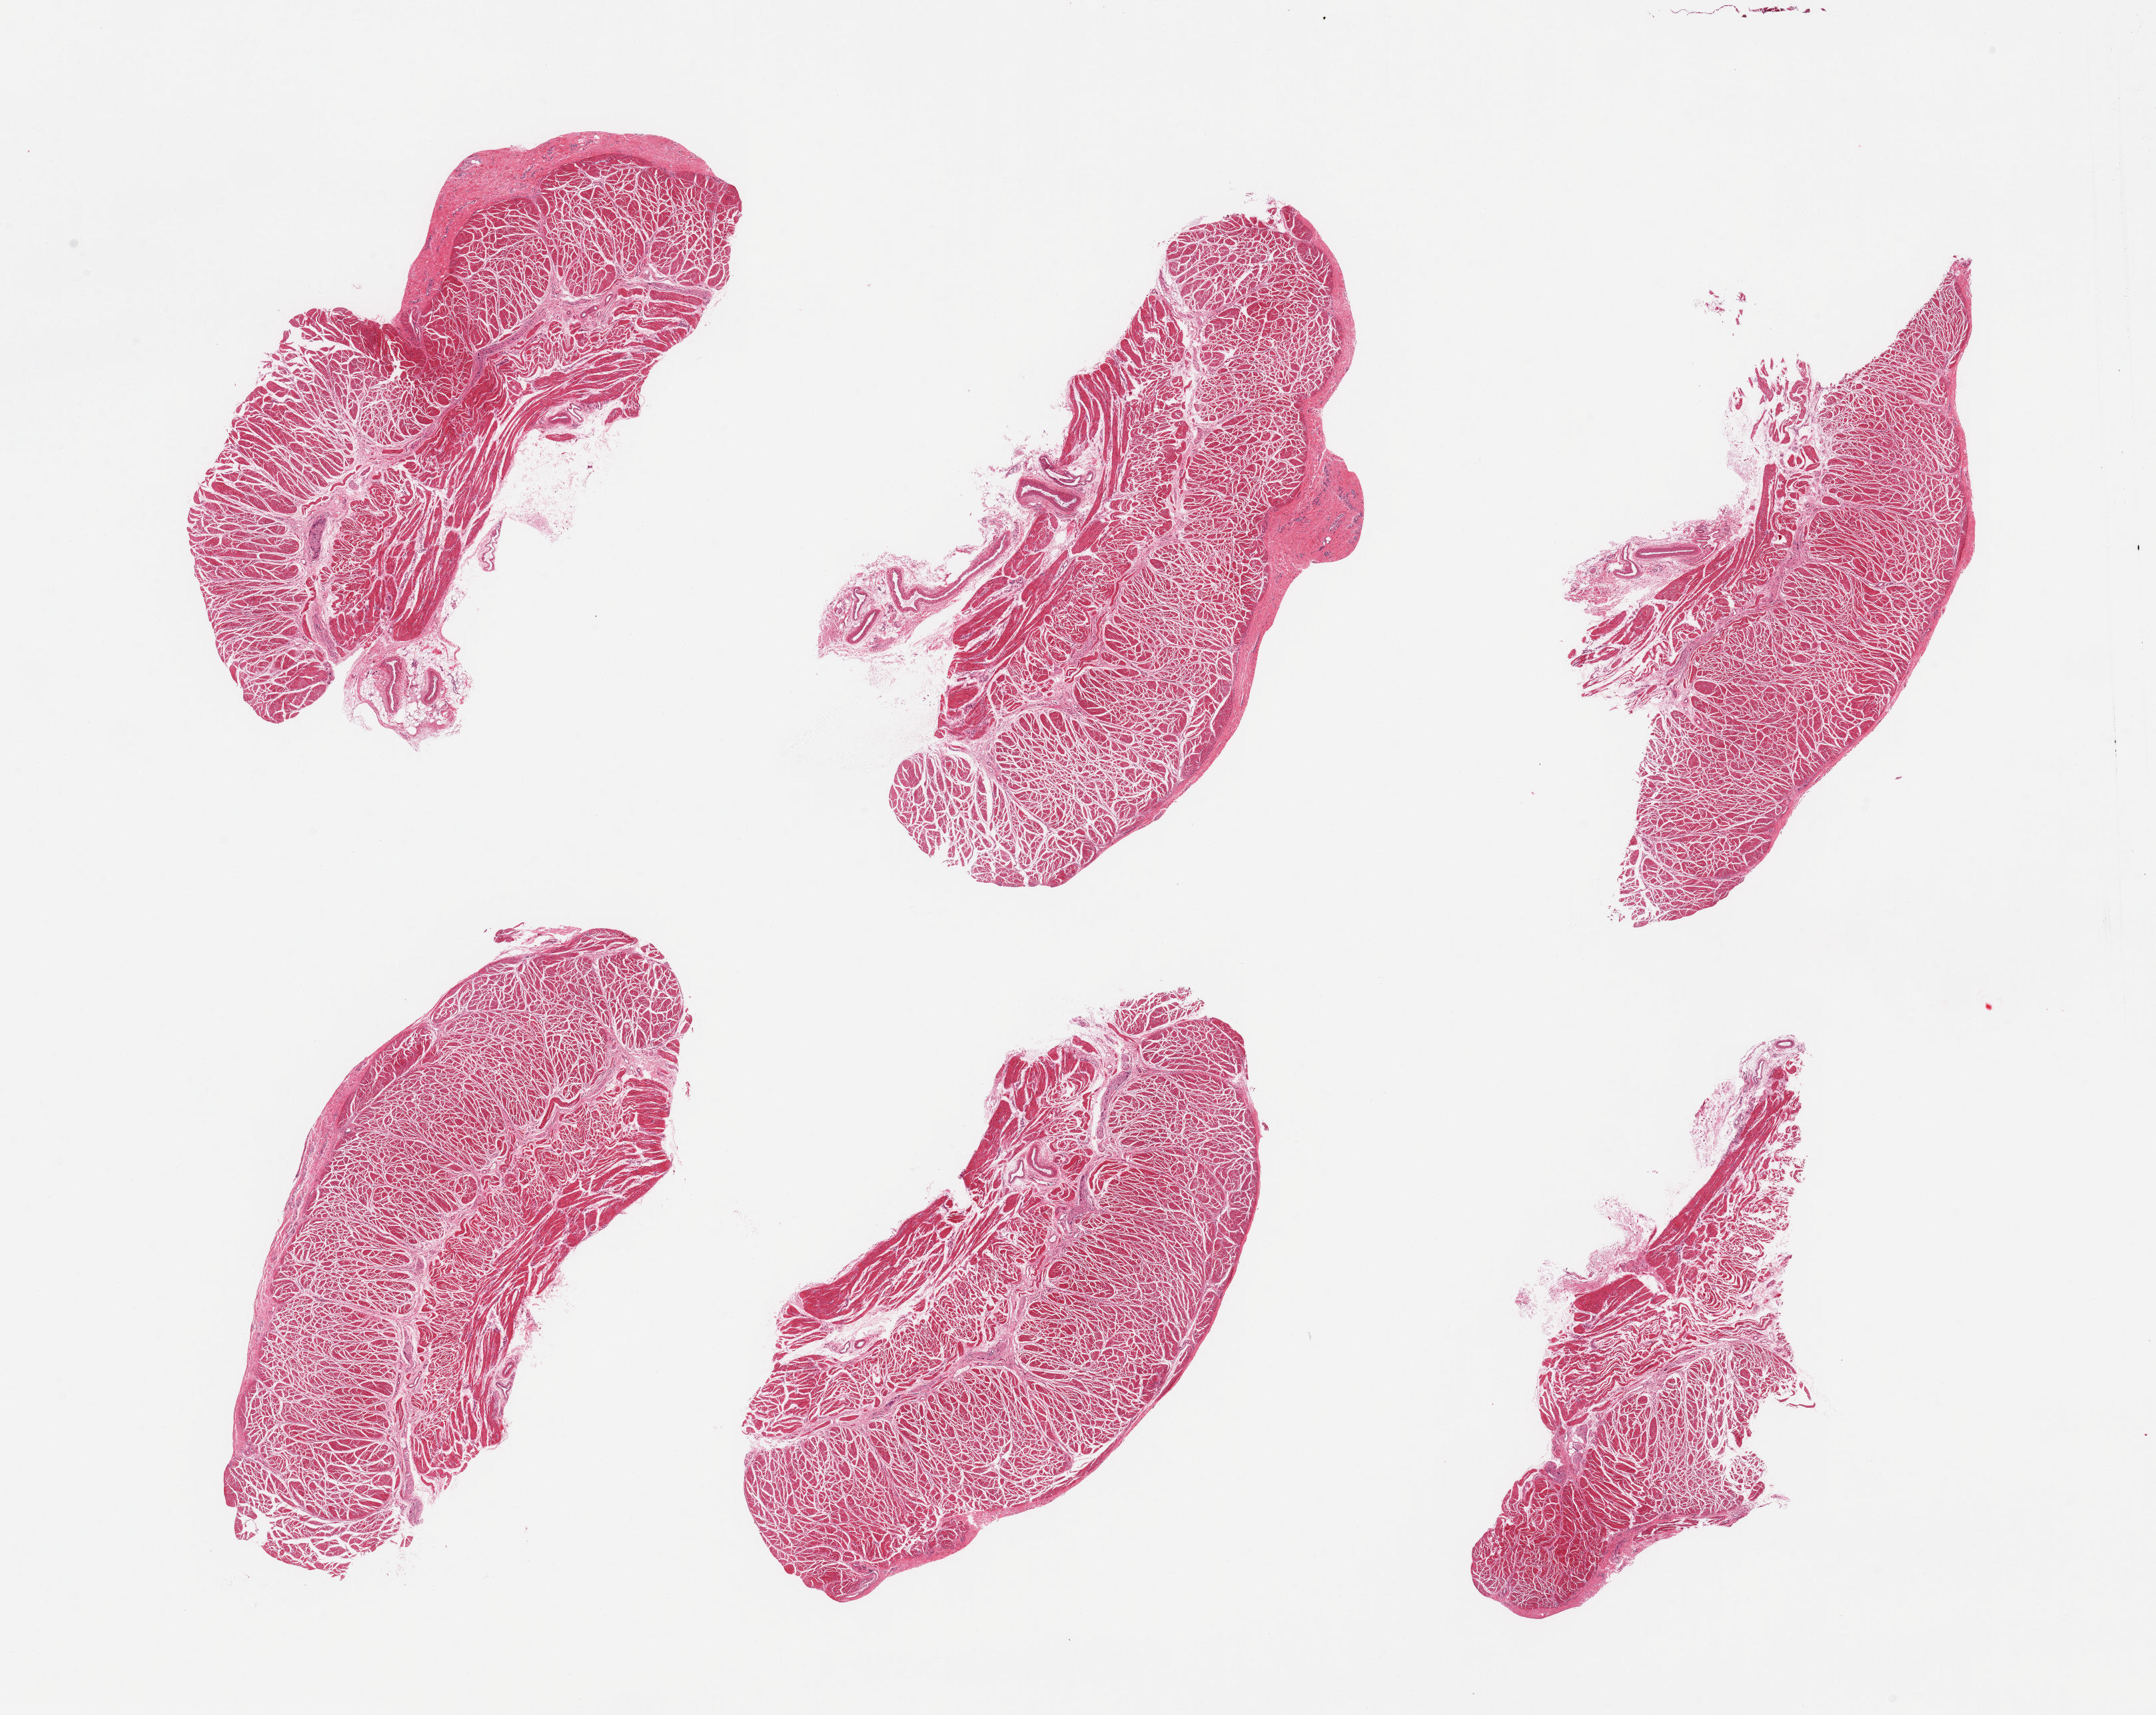
Haematoxylin and eosin whole-slide image, whole scanned area (about 25.6 x 20.4 mm) shown as a low-resolution overview; PAXgene-fixed, paraffin-embedded tissue; sampled site (target tissue): esophageal muscle; tissue donor sample.
Reviewer comment on this tissue sample: 6 pieces; target muscularis, attached vessels/fat.